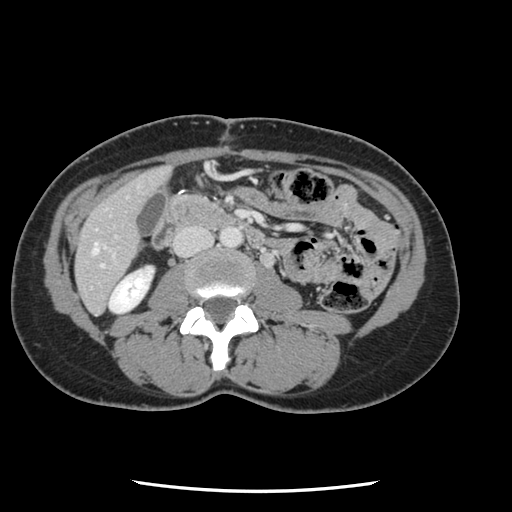
Contrast-enhanced abdominal CT, one axial slice. Position 23 of 134 along the scan axis. 120 kVp. Intravenous contrast given. Soft-tissue window (W 400 / L 40 HU). 512 × 512 image matrix, field of view 330 × 330 mm. Female patient, age 43 years. Case-level facts recorded for this patient, not image findings: diagnosis: colorectal cancer liver metastases, imaged before liver resection.
Annotated regions visible in this slice (expert manual segmentation):
- hepatic veins: bounding box [x1, y1, x2, y2] px = [93, 243, 98, 254]
- liver: [76, 168, 170, 313]
- planned liver remnant (the part of the liver to remain after resection): [76, 168, 170, 313]